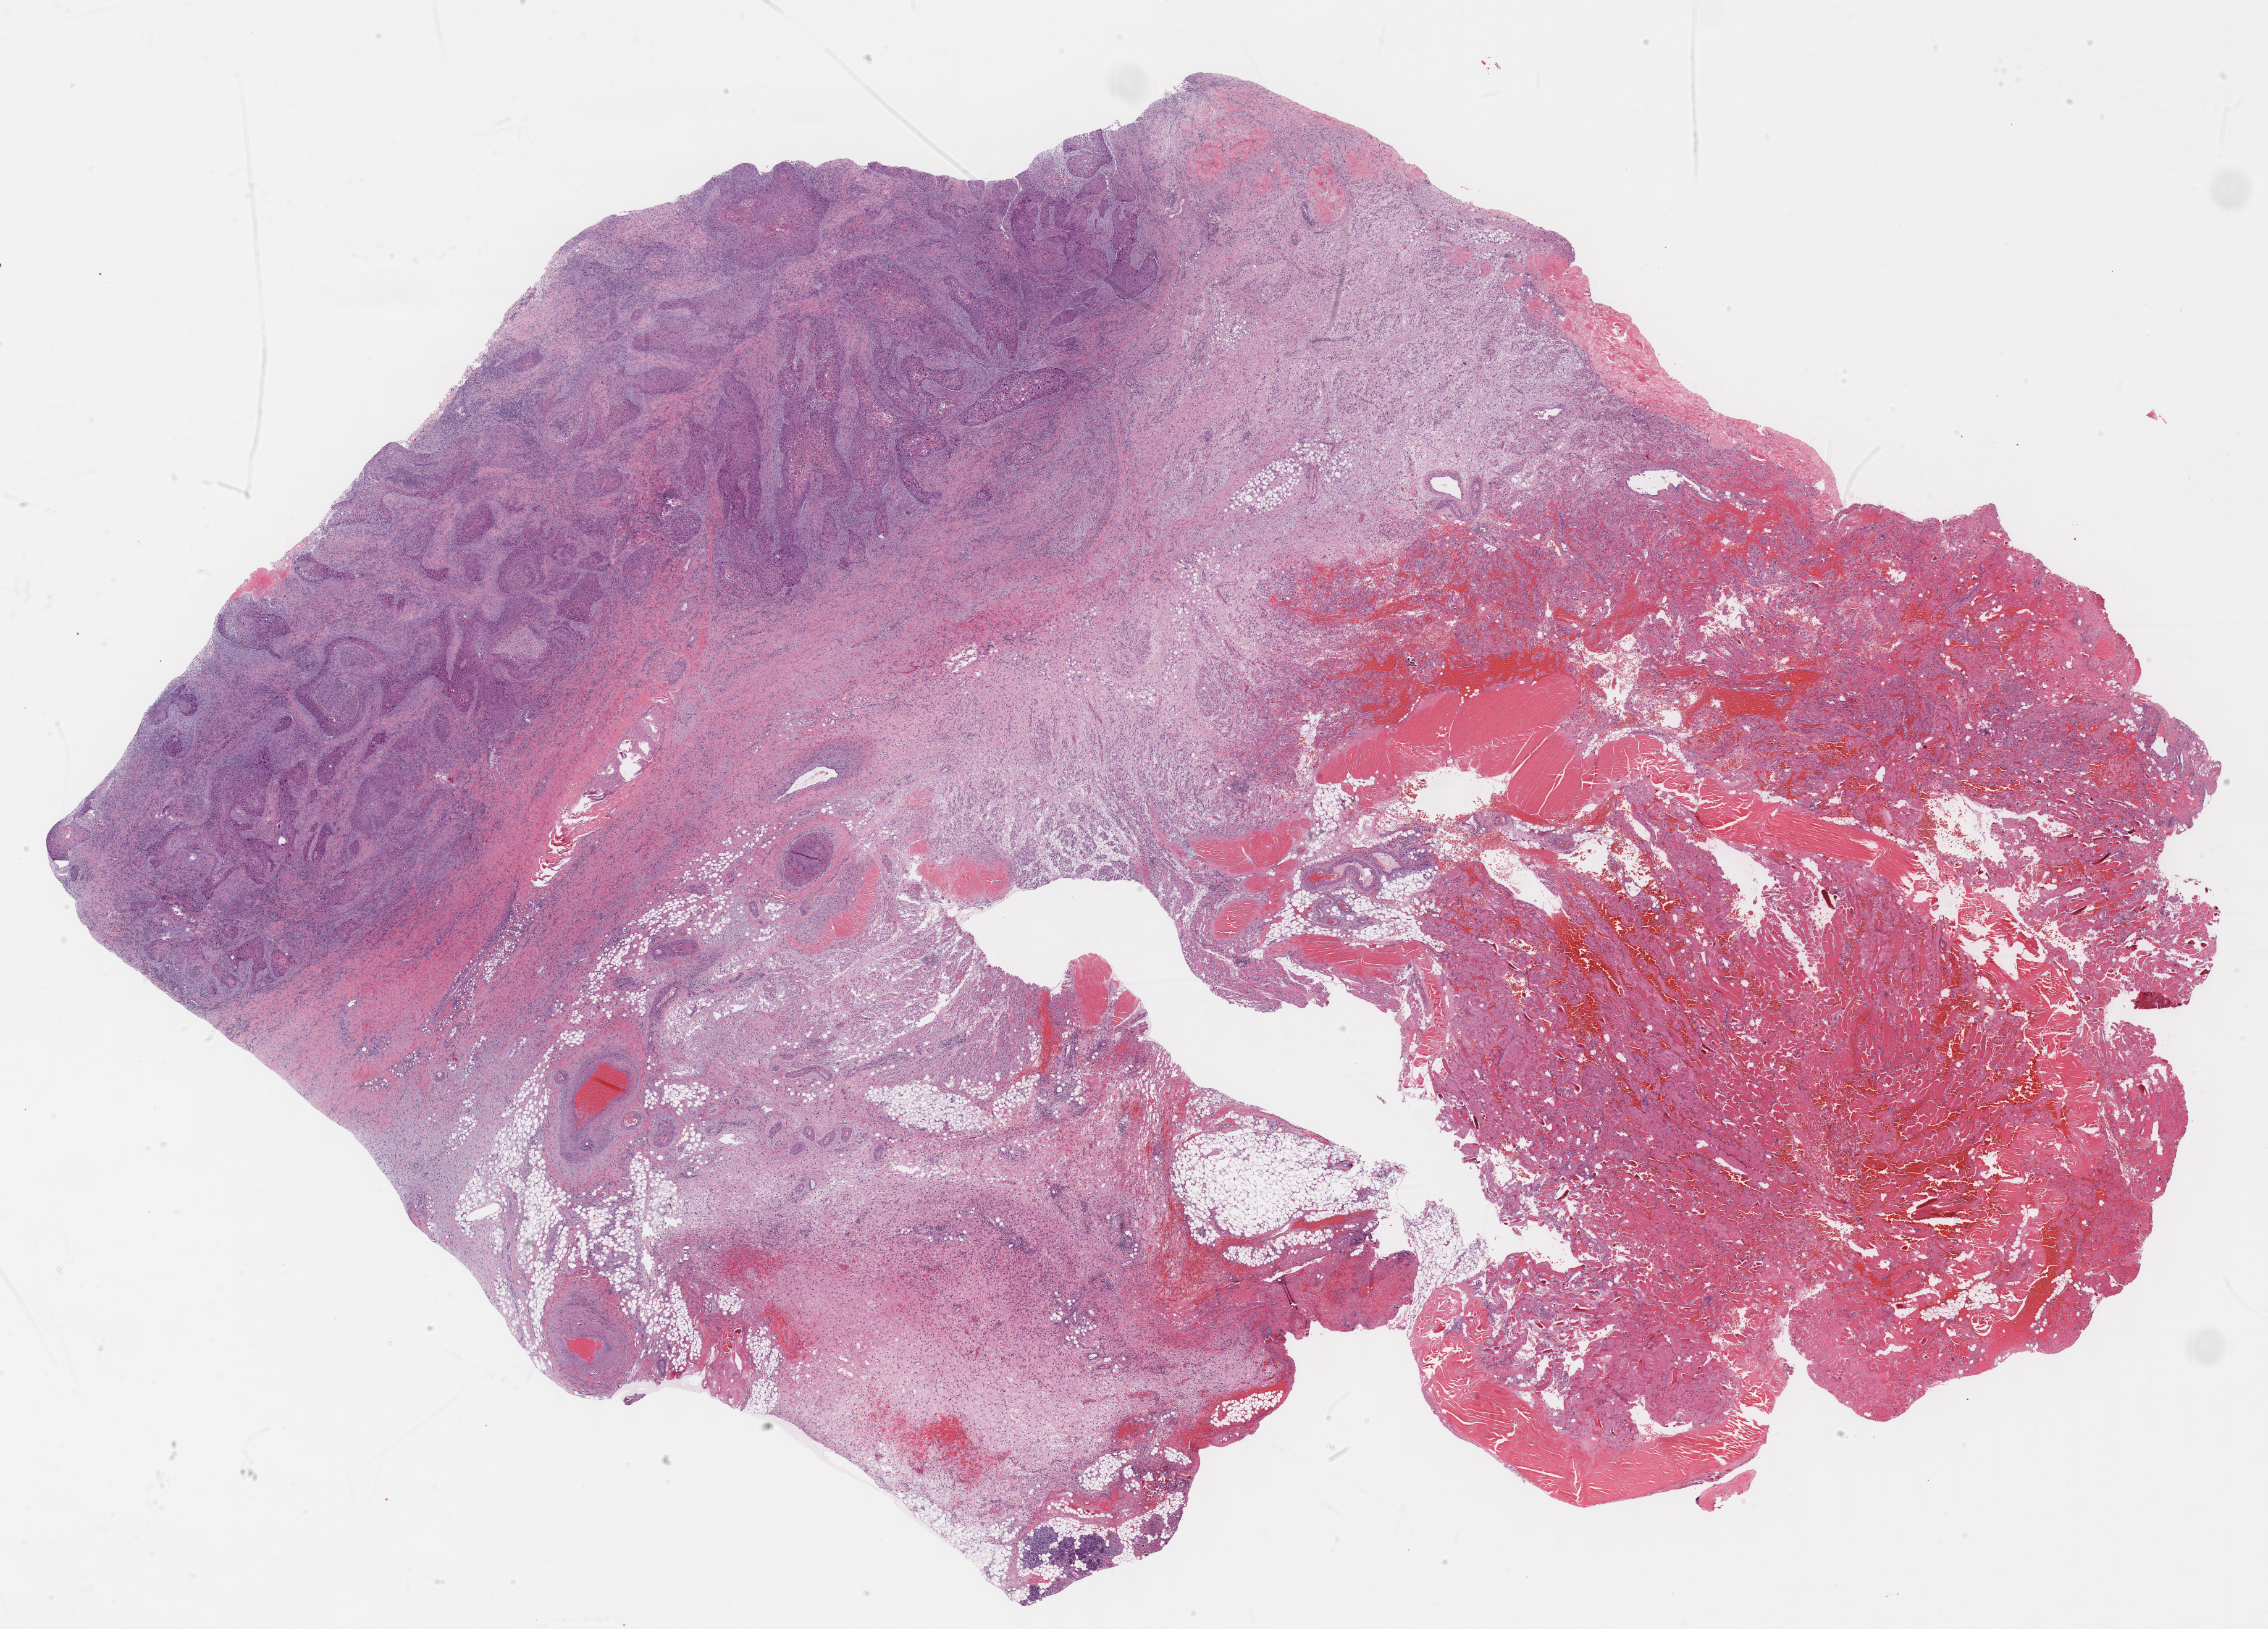
Whole-slide histology image, H&E, shown as a low-resolution overview of the whole scanned area (about 29.7 x 21.3 mm); formalin-fixed paraffin-embedded (FFPE) diagnostic section; head and neck, primary tumour sample. Male patient; age at initial diagnosis 79 years.
Diagnosis: Squamous cell carcinoma, NOS.